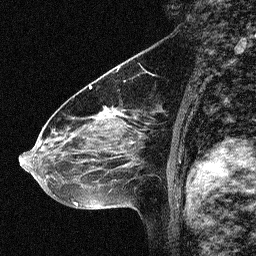
Breast MRI (dynamic contrast-enhanced), one sagittal slice; slice 38 of 64 in the series (ordered by position); dynamic contrast-enhanced study with each time point stored as its own series, time point 2 of 3 at this slice position (early post-contrast, ordered by acquisition time); 1.5 T; TE 4.5 ms, TR 11 ms; 256 × 256 image matrix, field of view 200 × 200 mm. Female patient, age 46 years. From the clinical record (not read from this slice): setting: breast cancer imaged before/during neoadjuvant chemotherapy; receptor status: HER2-positive.
Annotated regions visible in this slice (semi-automatic segmentation, software-assisted and operator-edited):
- analysis volume of interest (the breast-tissue region the enhancement analysis was run in; not a lesion): box from (x=42, y=80) to (x=150, y=180) px
- tumour enhancement mask (voxels above the 90 % enhancement threshold inside the analysis volume of interest): (x=91, y=110)–(x=141, y=155)